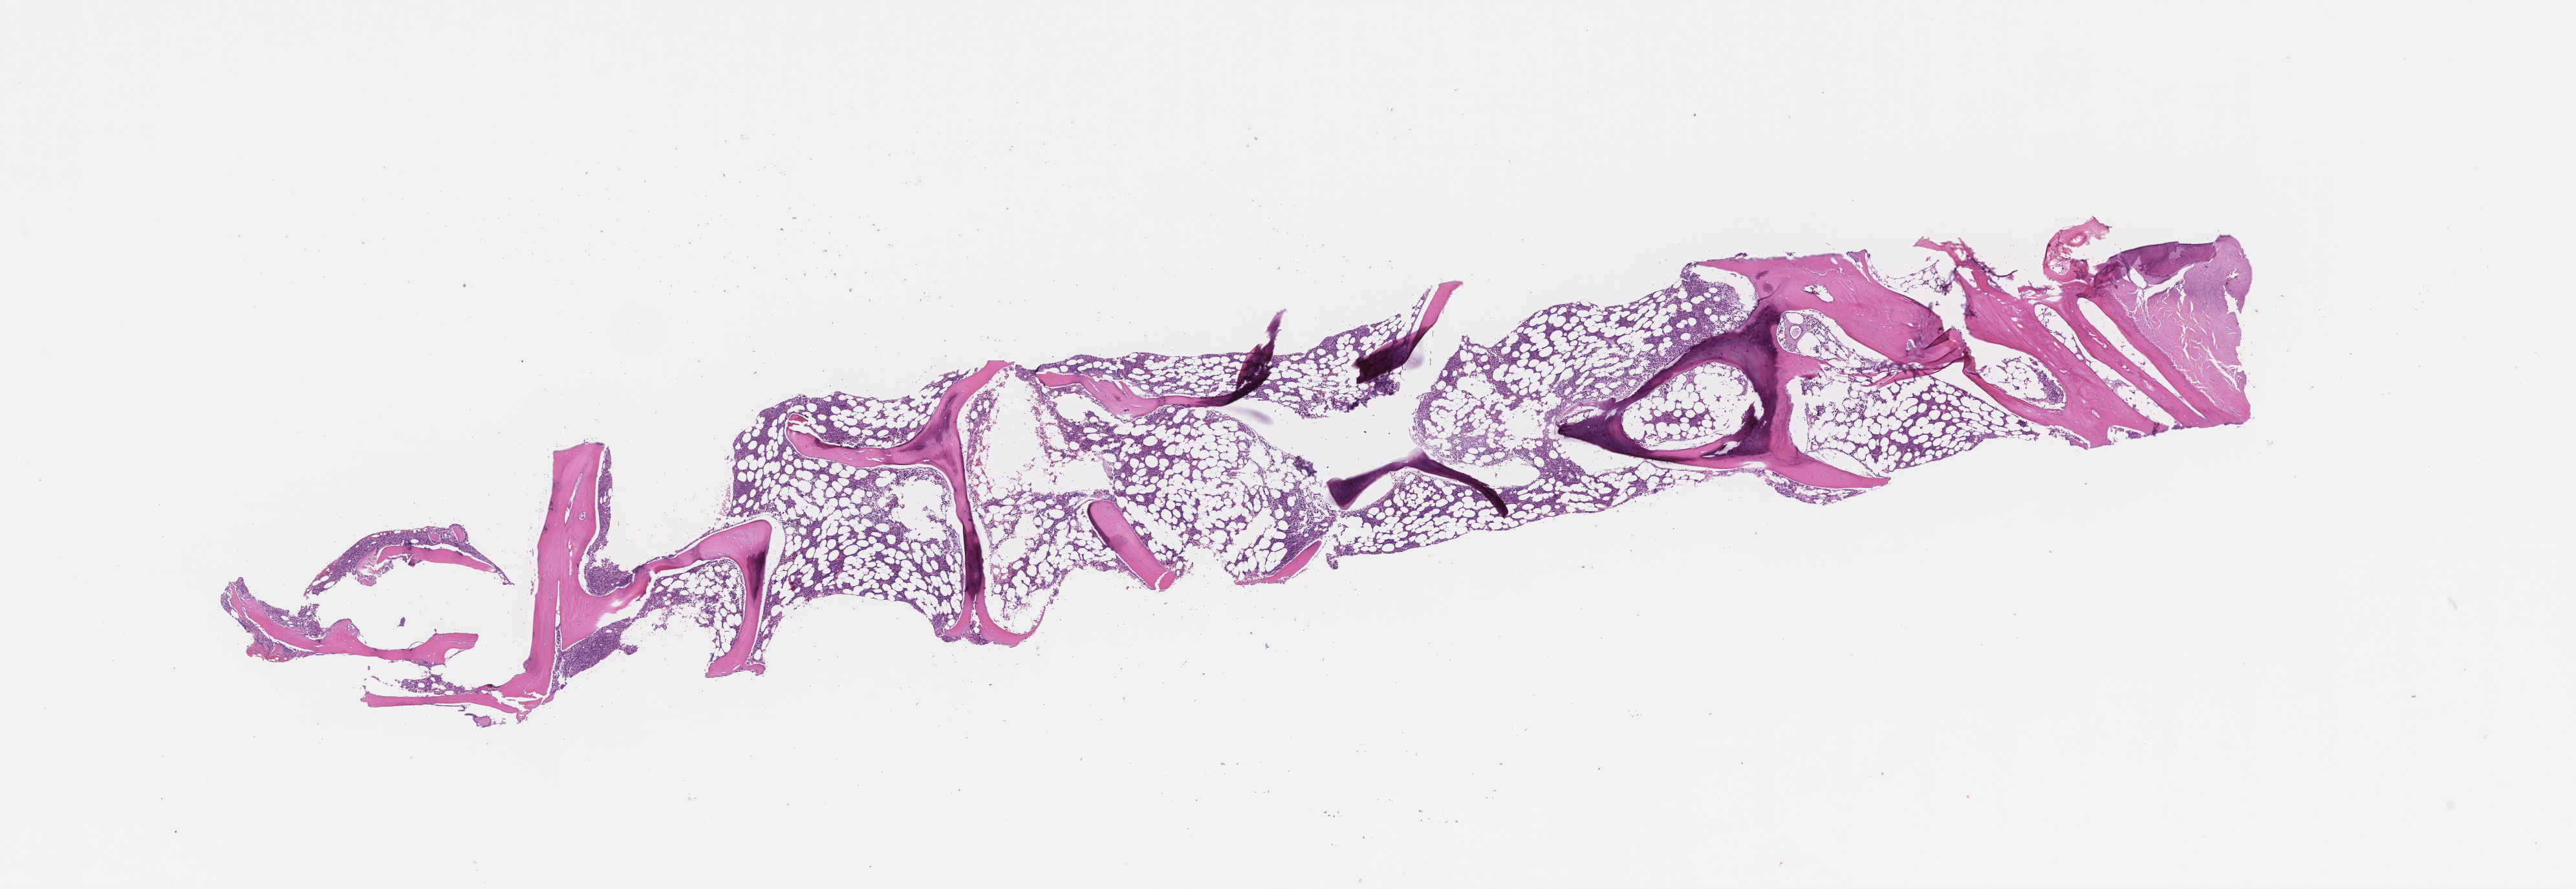
Digitized hematoxylin and eosin (H&E)-stained section, low-resolution overview of the scanned area, about 16.1 x 5.5 mm. Formalin-fixed, paraffin-embedded (FFPE) tissue. Tissue site: bone marrow. Specimen time point: archival tissue. Patient: female.
This section: primary tumor. Diagnosis: Plasma Cell Myeloma.